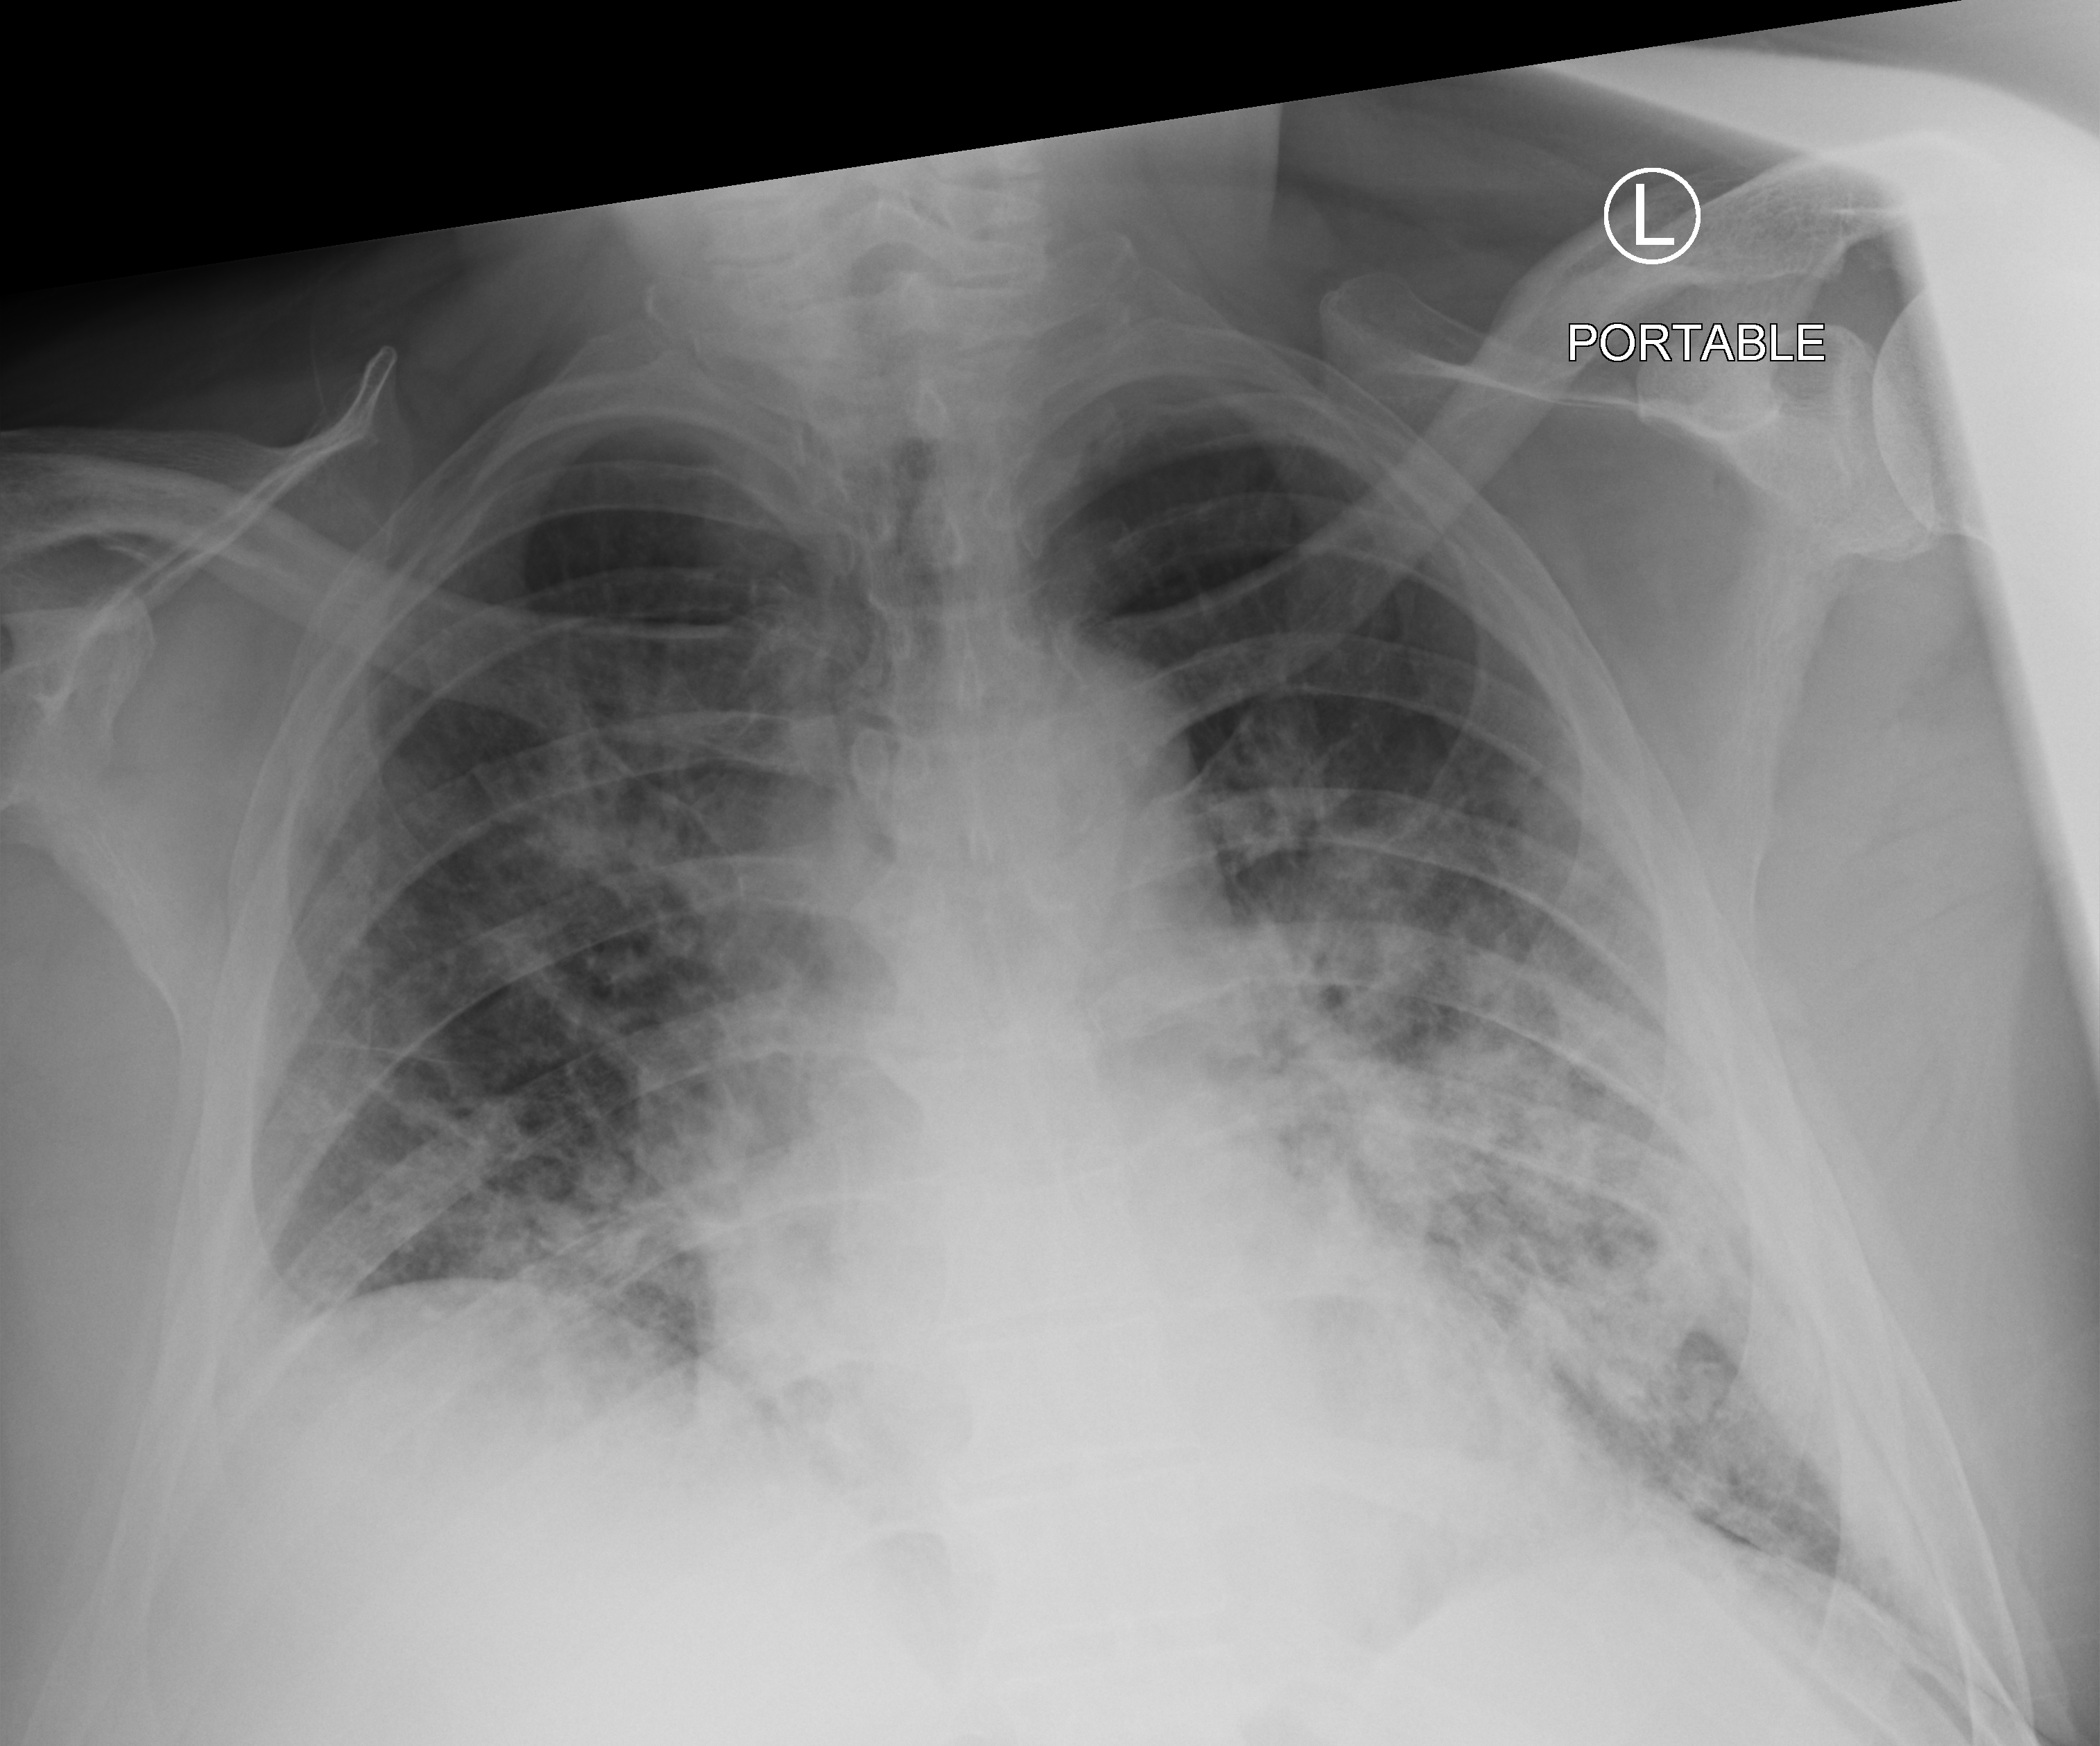
Chest X-ray (portable), anteroposterior (AP) projection. Male patient hospitalised with COVID-19, age 60–74 years.
From the hospital-stay record, not from the radiograph (when in the stay this image was taken is not recorded):
- mechanically ventilated during this hospital stay: no
- admitted to intensive care during this hospital stay: no